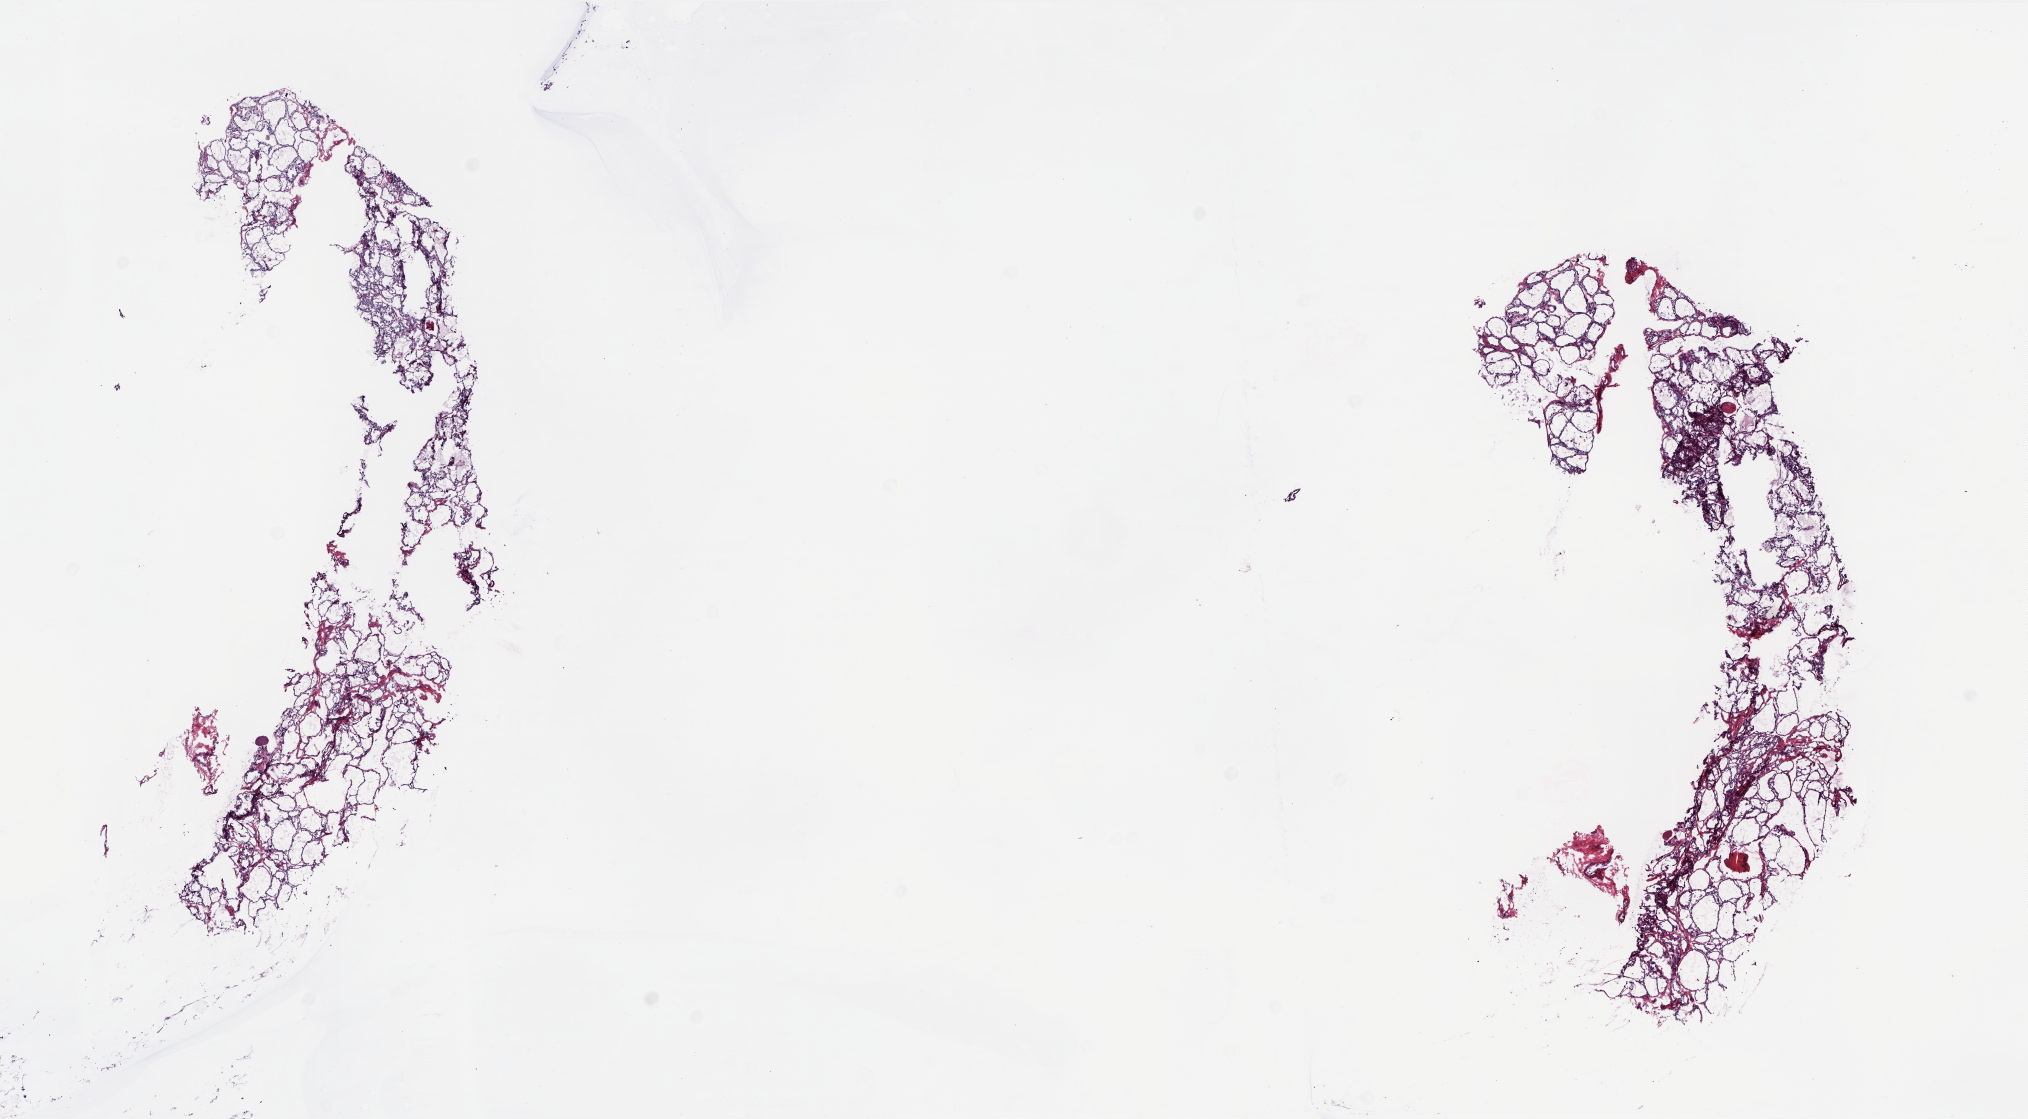
Digitized Hematoxylin and eosin (H&E) stained tissue section (whole slide), whole scanned area (about 16.4 x 9.0 mm) shown as a low-resolution overview. Frozen section. Solid tissue normal (non-tumour tissue) sample from the thyroid. Female, age 51 years at initial diagnosis. Composition of this section per pathologist review: tumour cells 0%, tumour nuclei 0%, normal cells 100%, stromal cells 0%, necrosis 0%. Inflammatory infiltration, as recorded: lymphocyte infiltration 0%, monocyte infiltration 0%, neutrophil infiltration 0%.
This section: solid tissue normal (non-tumour) sample from the same patient. Patient diagnosis: Papillary carcinoma, follicular variant (thyroid gland).